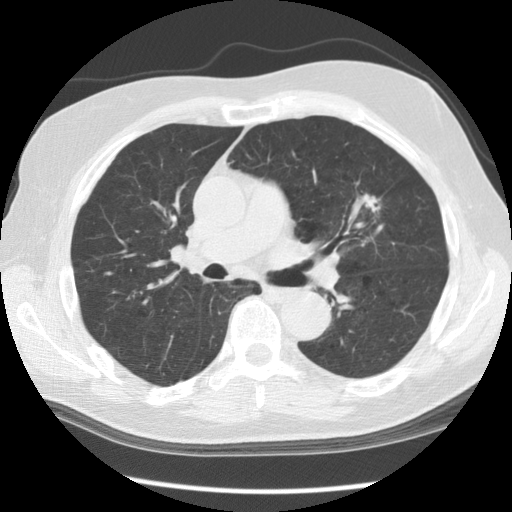
Axial slice from a low-dose chest CT screening exam; second screening round (one year after baseline); lung window (W 1500 / L -600 HU); 2.5 mm slice thickness; slice 82 of 140 in the series; 512 × 512 image matrix. Male participant, aged 70 years at enrolment.
Expert-annotated lung lesion, bounding box [x1, y1, x2, y2] px = [340, 178, 399, 233]. The screening reader recorded 3 non-calcified nodules or masses ≥4 mm on this exam (right lower lobe, left upper lobe, left upper lobe); which of them this box marks is not recorded. Lung cancer was diagnosed 396 days after this screen (after the third annual screen): adenocarcinoma, NOS, left upper lobe, moderately differentiated (G2), stage IIIA (AJCC 6th edition), 17 mm at pathology.